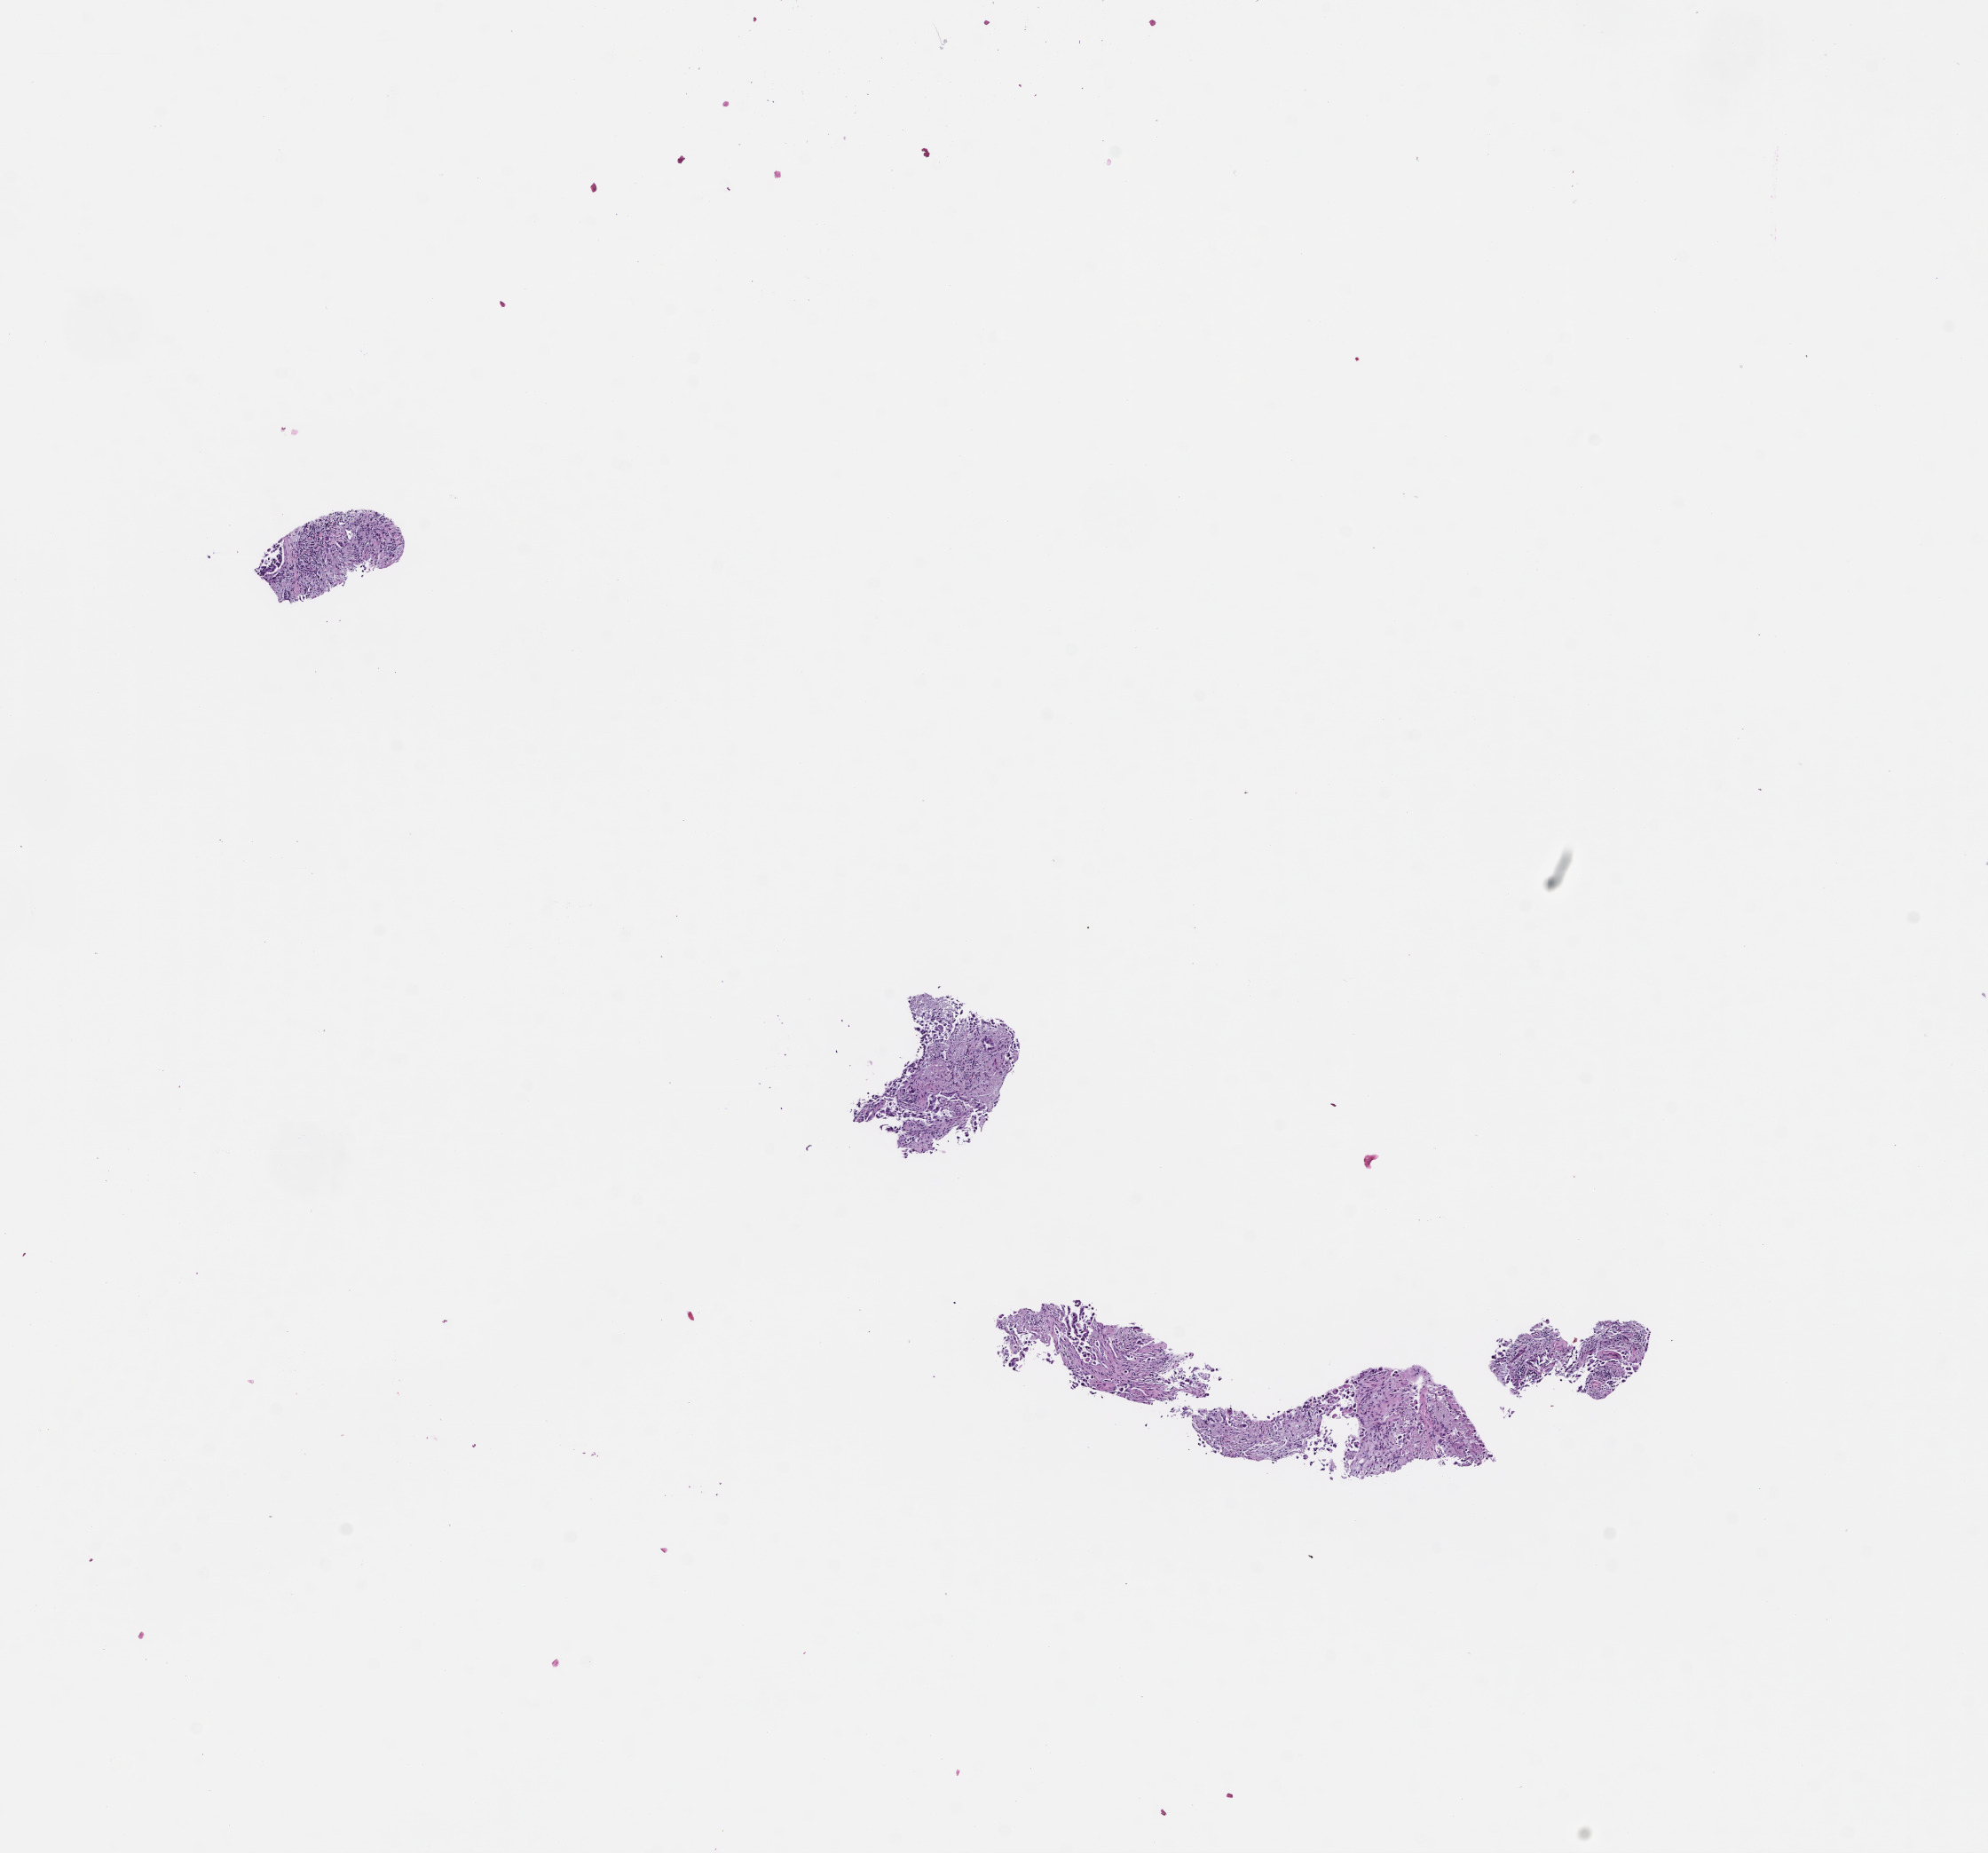
Whole-slide image, hematoxylin and eosin (H&E) stain, low-resolution overview of the scanned area, about 9.0 x 8.4 mm. Formalin-fixed, paraffin-embedded (FFPE) tissue. Site: lung. Specimen time point: collected at baseline (before treatment). Patient: female.
* this section: primary tumor
* diagnosis: Non-Small Cell Lung Carcinoma